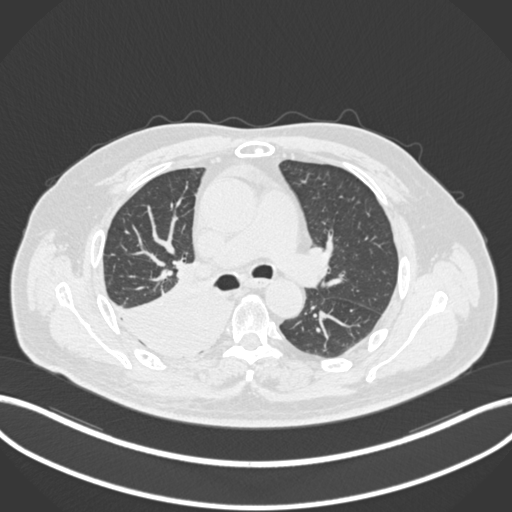
Chest CT, one axial slice. Slice 123 of 218 in the series (ordered by position). Reconstruction kernel B30f. 120 kVp. Lung window (W 1500 / L -600 HU). 1 mm slice thickness. 512 × 512 image matrix, field of view 400 × 400 mm. Male patient, age 68 years. From the clinical record (not read from this slice): clinical TNM (as recorded): T2a N0 M0.
Annotated regions visible in this slice (bounding box drawn by a radiologist):
- lung tumour (recorded histology: adenocarcinoma): bounding box (x1, y1, x2, y2) in pixels: (112, 274, 231, 364)